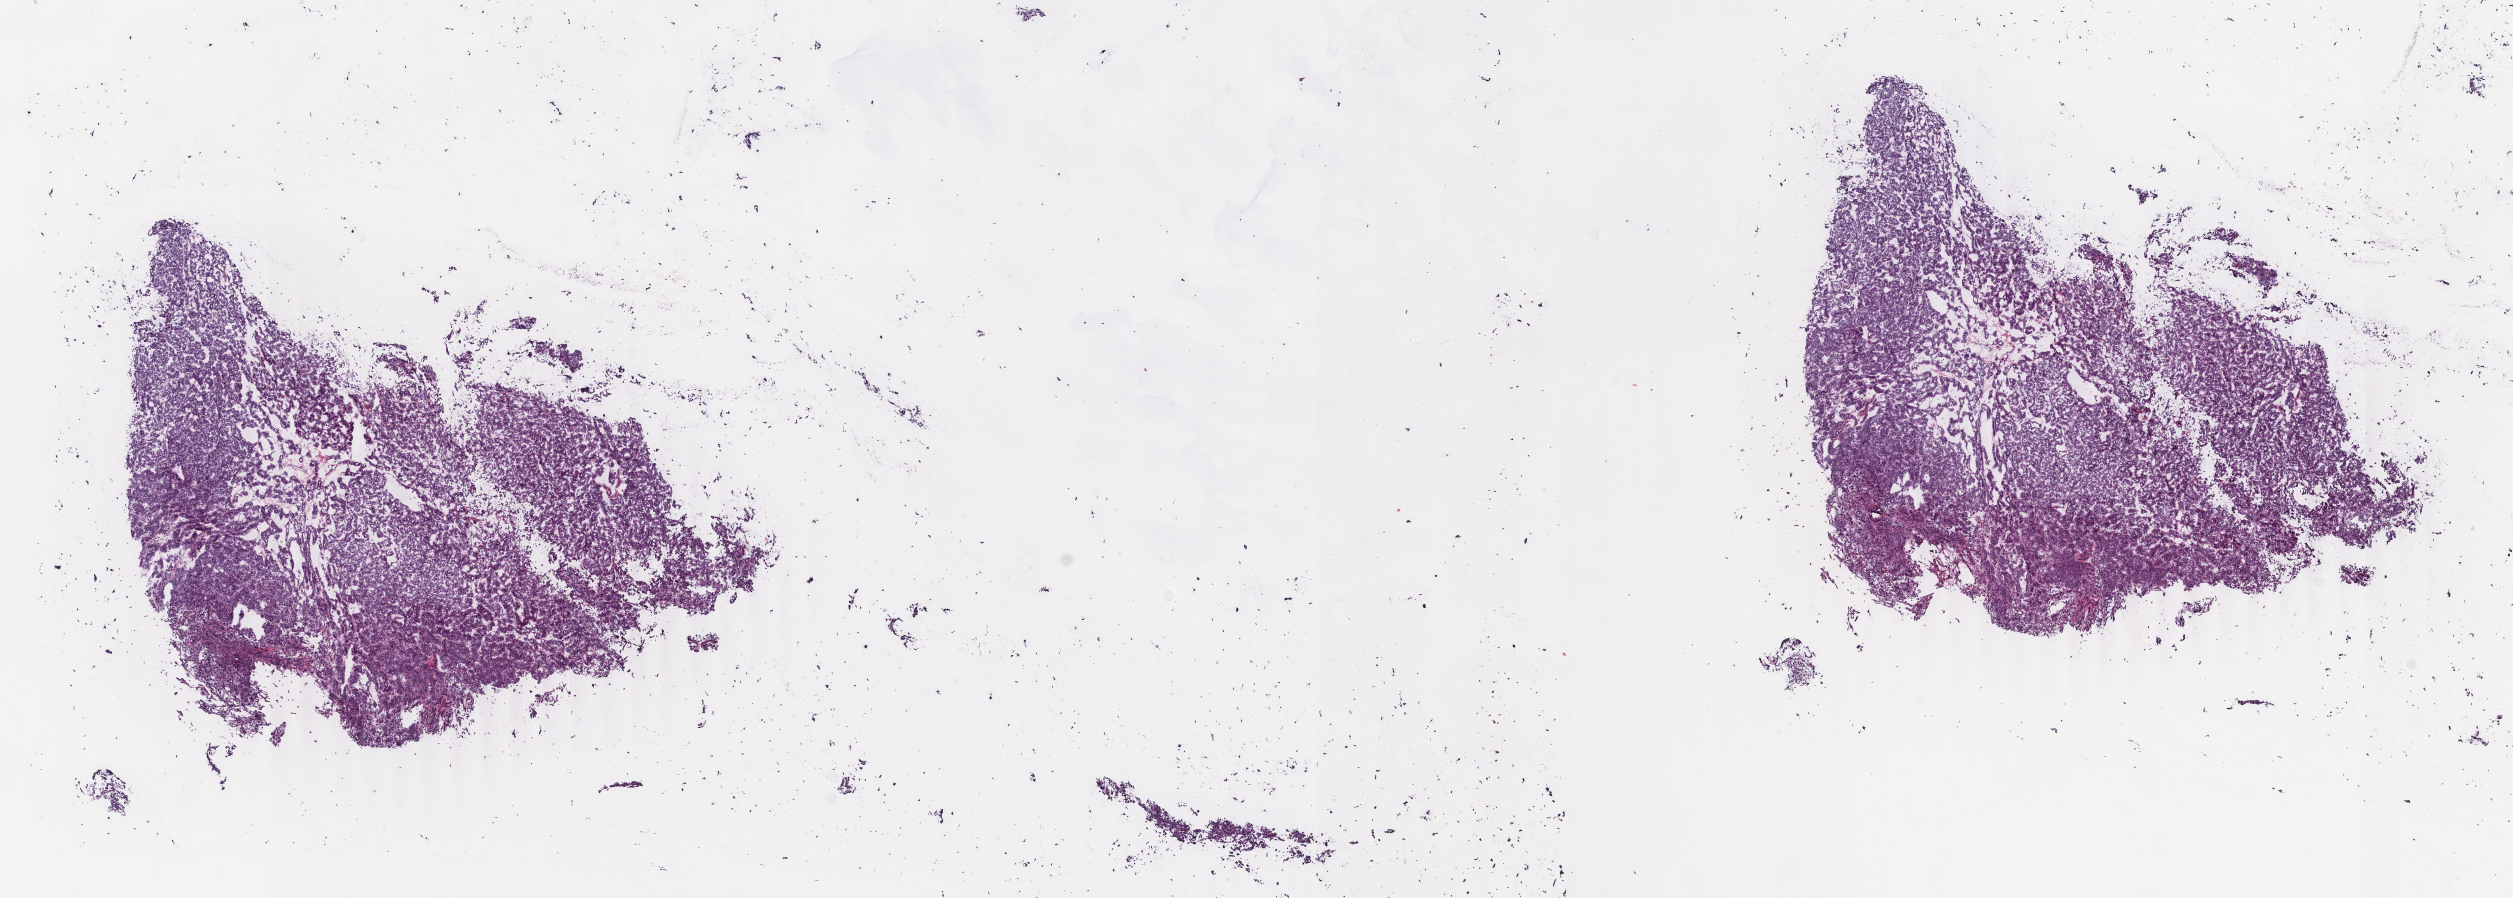
Whole-slide histology image, Hematoxylin and eosin (H&E) stained — shown as a low-resolution overview of the whole scanned area (about 20.0 x 7.1 mm). Frozen section. Sample: primary tumour, thyroid. Female, age 56 years at initial diagnosis. Slide review estimates, as recorded: tumour cells 100%, tumour nuclei 90%, normal cells 0%, stromal cells 0%, necrosis 0%. Inflammatory infiltration, as recorded: lymphocyte infiltration 0%, monocyte infiltration 0%, neutrophil infiltration 0%.
* AJCC pathologic stage: II (7th edition)
* laterality: left
* diagnosis: Papillary carcinoma, follicular variant
* lymph nodes positive (case pathology): 0 of 1 examined